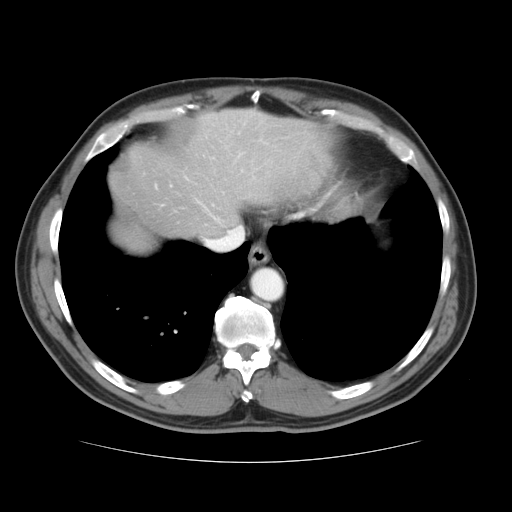
Contrast-enhanced abdominal CT, one axial slice. Position 32 of 37 along the scan axis. Intravenous contrast given. Soft-tissue window (W 400 / L 40 HU). 5 mm slice thickness. 512 × 512 image matrix, field of view 374 × 374 mm. Male patient, age 66 years. From the clinical record (not read from this slice): diagnosis: colorectal cancer liver metastases, imaged before liver resection; multiple liver metastases: yes; largest metastasis: 1.6 cm.
Structures marked on this image (outlined manually by an expert reader):
- hepatic veins: bounding box <195,199,241,241> (left, top, right, bottom; pixels)
- liver: <109,109,337,254>
- planned liver remnant (the part of the liver to remain after resection): <113,112,338,254>